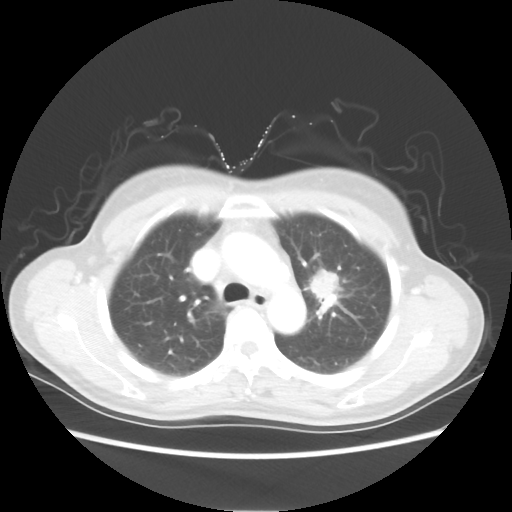
Chest CT, one axial slice. Position 39 of 54 along the scan axis. Reconstruction kernel STANDARD. 80 kVp. Lung window (W 1500 / L -600 HU). 5 mm slice thickness. 512 × 512 image matrix, field of view 360 × 360 mm. Patient: female, 53 years. Case-level facts recorded for this patient, not image findings: clinical TNM (as recorded): T1c N0 M0.
Annotated regions visible in this slice (rectangle marked by the reading radiologist):
- lung tumour (recorded histology: adenocarcinoma): bounding box <302,259,347,306> (left, top, right, bottom; pixels)
- lung tumour (recorded histology: adenocarcinoma): <305,263,340,303>